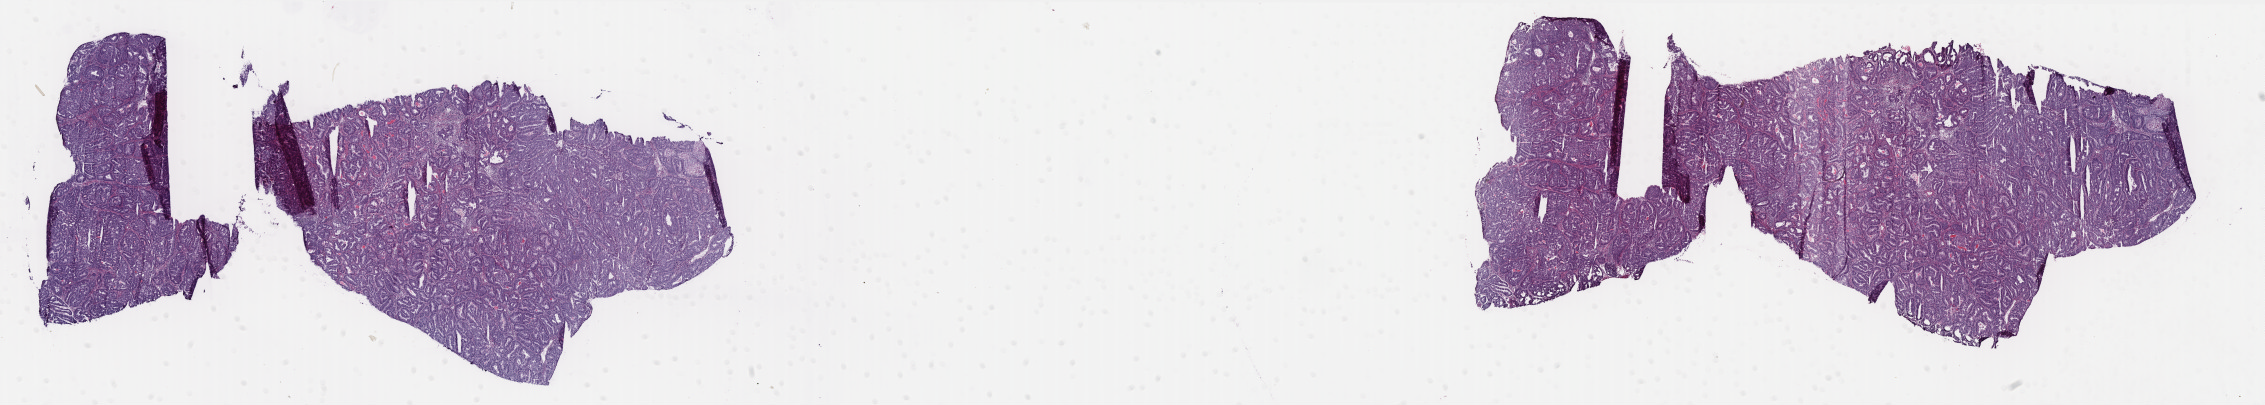
Hematoxylin and eosin (H&E) stained whole-slide image, a low-resolution overview of the entire scanned area, about 36.3 x 6.5 mm (slide scanned at 40x). Frozen section. Uterus, primary tumour sample. Female, age 57 years at initial diagnosis. Histologic grade: G1 (well differentiated). Slide review estimates, as recorded: tumour cells 85%, tumour nuclei 85%, normal cells 0%, stromal cells 15%, necrosis 0%. Inflammatory infiltration, as recorded: lymphocyte infiltration 0%, monocyte infiltration 0%, neutrophil infiltration 0%.
• FIGO stage: IB
• diagnosis: Endometrioid adenocarcinoma, NOS (endometrium)